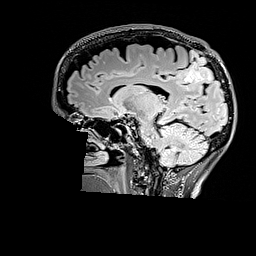
Brain MRI from a brain-tumour surgery series, one sagittal slice; T2 FLAIR; 1 mm slice thickness; 256 × 256 image matrix, field of view 256 × 256 mm. From the clinical record (not read from this slice): histopathology: Astrocytoma; WHO grade: 3; IDH mutation: yes.
Outlined on this slice (outlined manually by an expert reader):
- tumour: bounding box (x1, y1, x2, y2) in pixels: (184, 50, 213, 82)
- tumour: (185, 57, 214, 83)